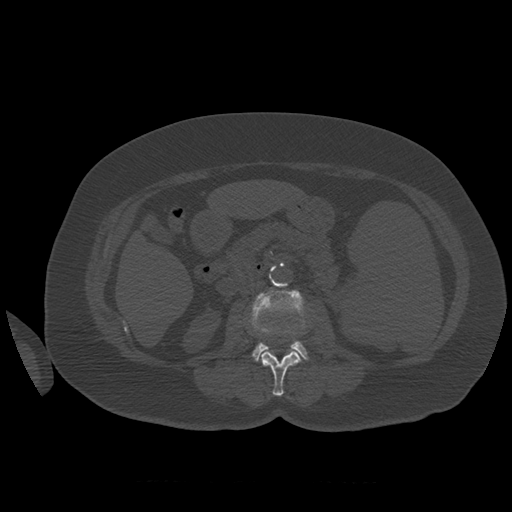
CT including the spine, one axial slice; position 243 of 399 along the scan axis; reconstruction kernel STANDARD; bone window (W 1800 / L 400 HU); 512 × 512 image matrix, field of view 404 × 404 mm. Patient age 81 years. Case-level facts recorded for this patient, not image findings: primary cancer: renal.
Outlined on this slice (semi-automatically segmented with operator editing):
- L2 vertebra: bounding box [x1, y1, x2, y2] px = [261, 330, 302, 397]
- L3 vertebra: [251, 289, 308, 362]